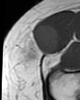
MRI of an extremity soft-tissue mass, one axial slice; position 16 of 46 along the scan axis; MR volume resampled by the dataset authors to the PET/CT grid (not the native acquisition matrix); 80 × 100 image matrix, field of view 78 × 98 mm. Female patient. Case-level facts recorded for this patient, not image findings: histological type: synovial sarcoma; grade: intermediate; site of the primary tumour: right thigh.
Annotated regions visible in this slice (expert contour drawn on MRI and transferred to this co-registered scan by the dataset authors):
- gross tumour volume including surrounding oedema: bounding box <23,24,59,59> (left, top, right, bottom; pixels)
- gross tumour volume (mass): <23,24,59,61>